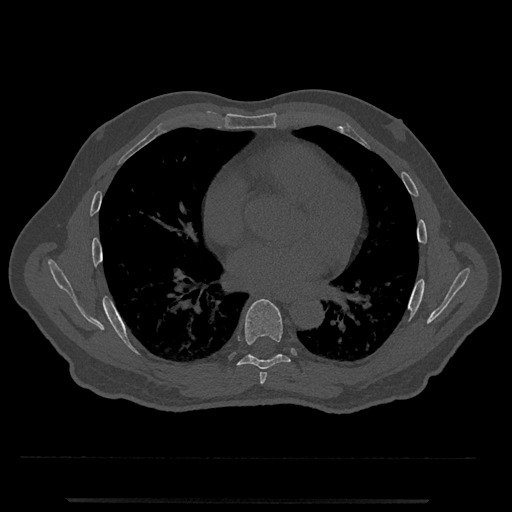
CT including the spine, one axial slice. Position 682 of 797 along the scan axis. Reconstruction kernel Br40s/3. 120 kVp. Bone window (W 1800 / L 400 HU). 512 × 512 image matrix, field of view 419 × 419 mm. Male patient, age 63 years. From the clinical record (not read from this slice): primary cancer: prostate.
Structures marked on this image (semi-automatic segmentation, software-assisted and operator-edited):
- T6 vertebra: bounding box <259,372,267,384> (left, top, right, bottom; pixels)
- T7 vertebra: <226,299,291,372>